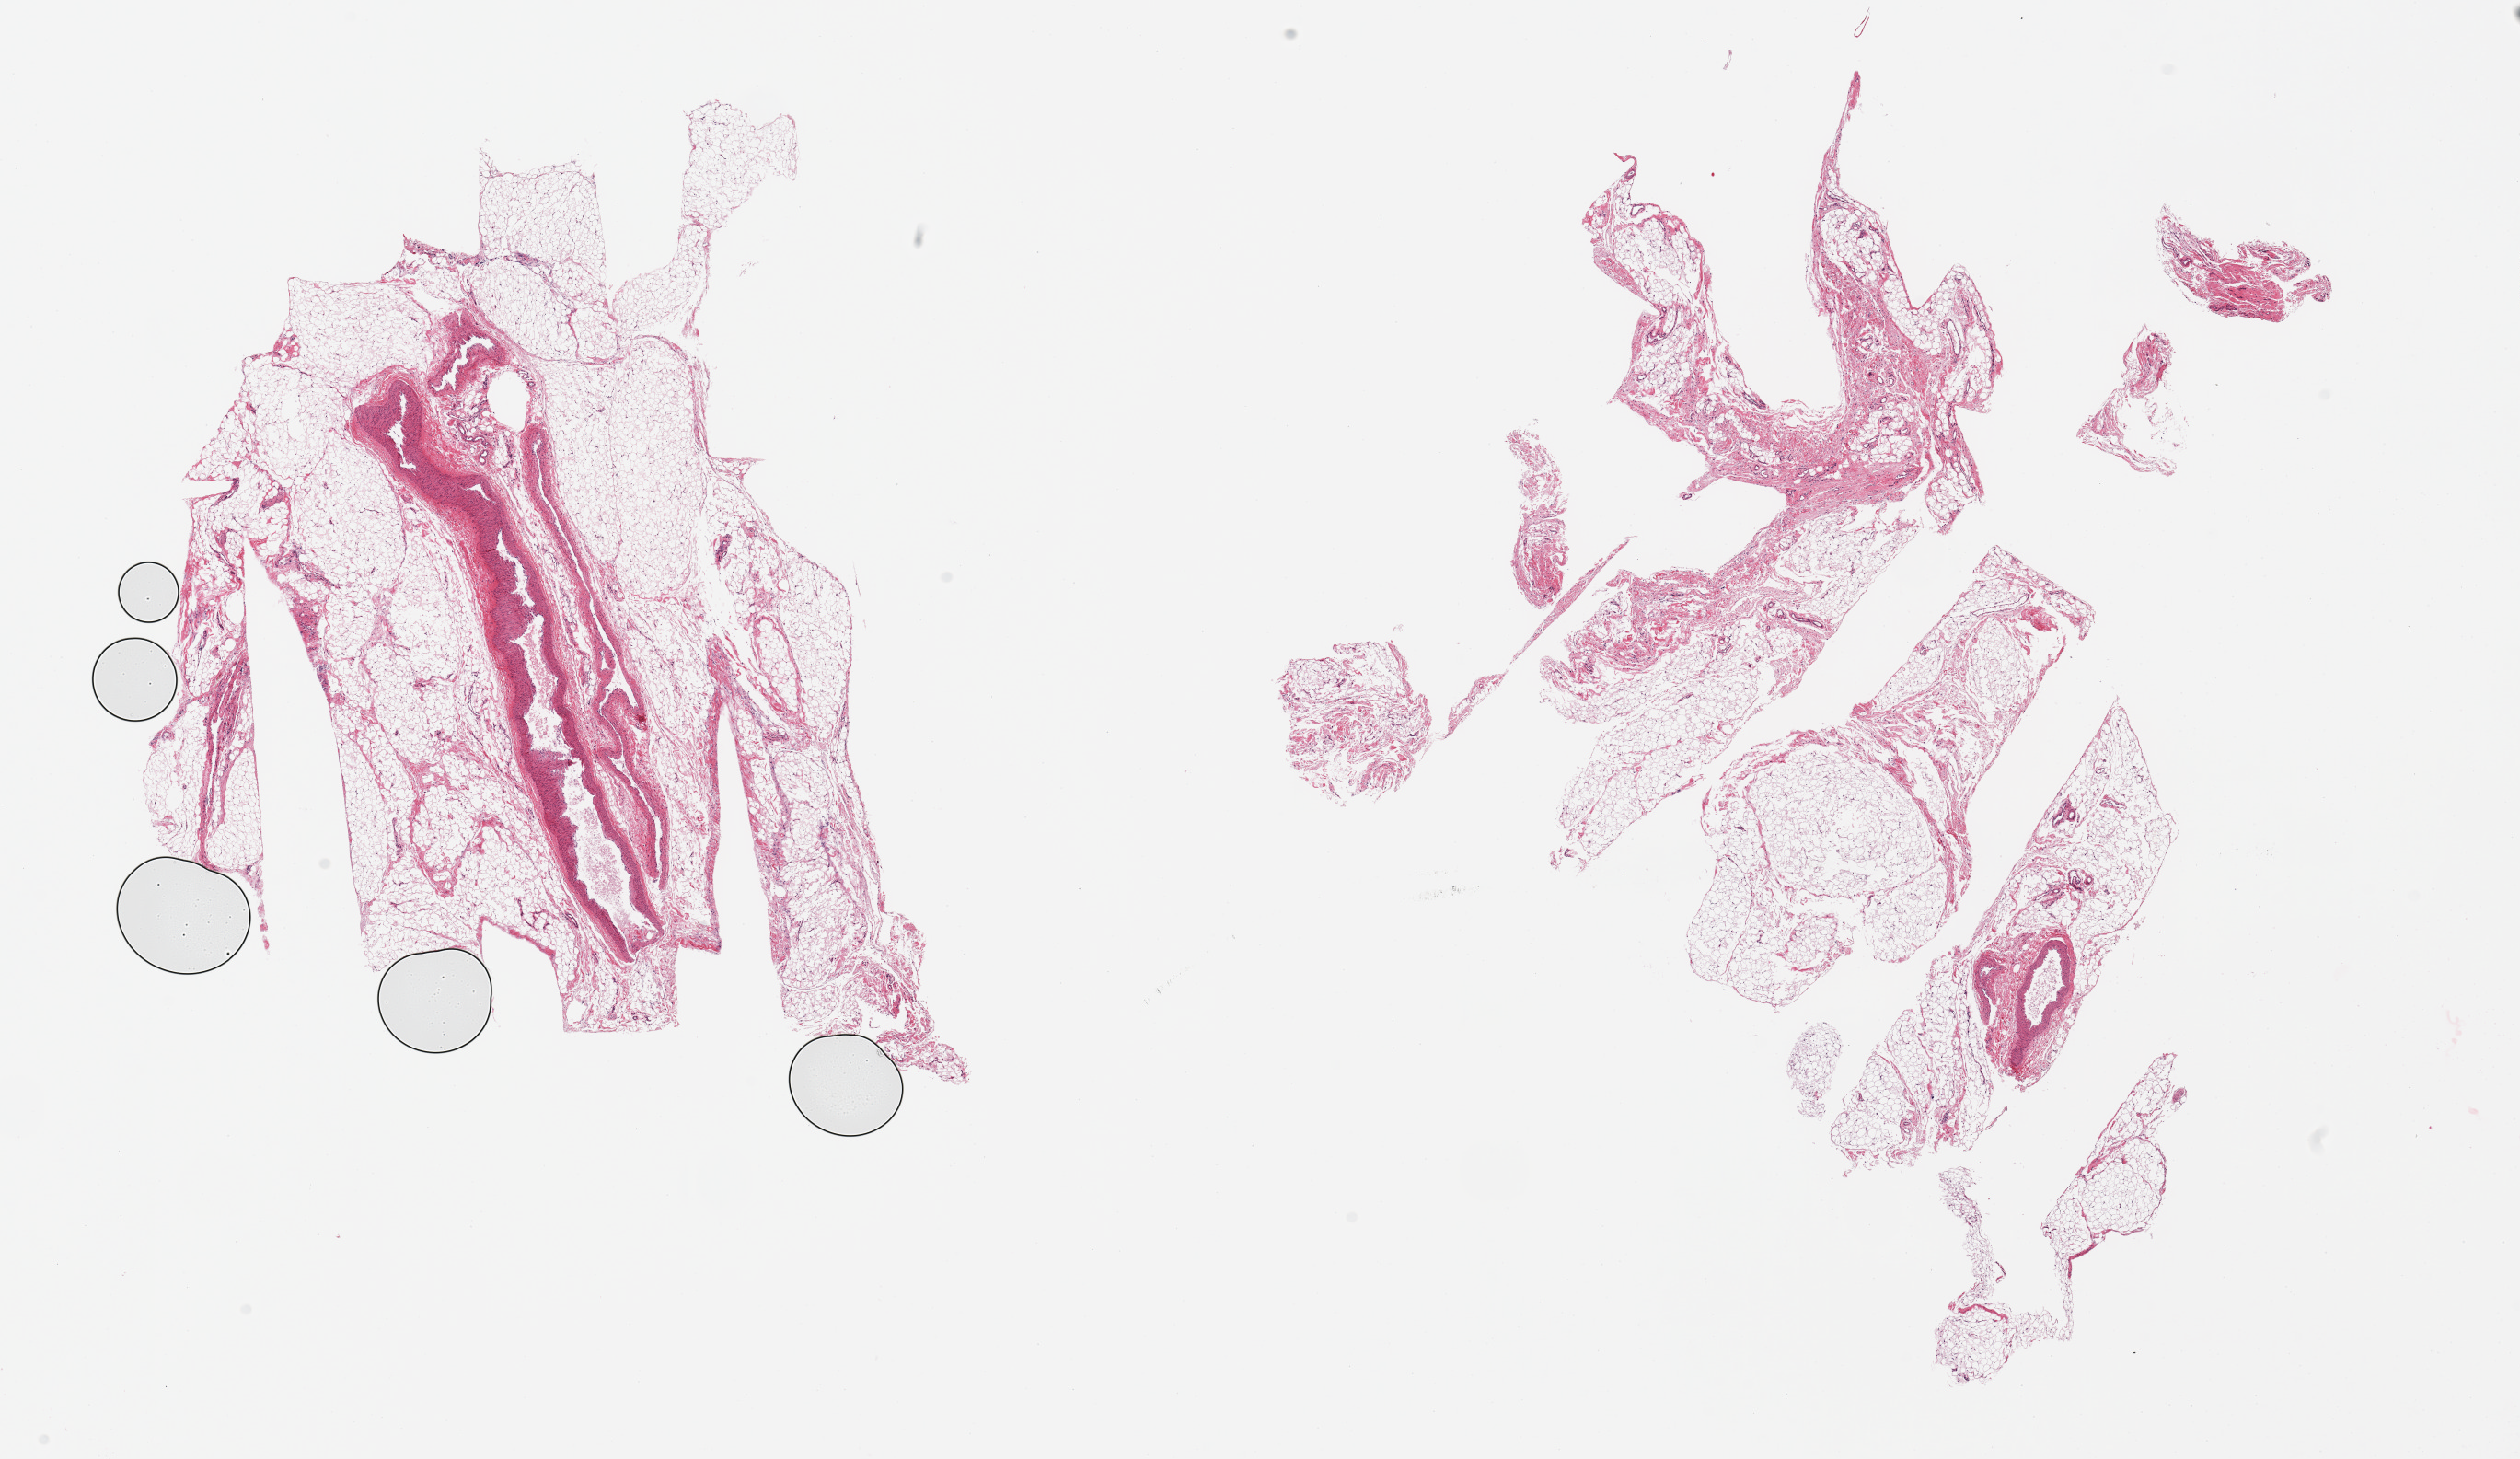
Whole-slide image, haematoxylin and eosin stain, a low-resolution overview of the entire scanned area, about 21.7 x 12.5 mm; PAXgene-fixed, paraffin-embedded tissue; section of omentum (target tissue); tissue donor sample.
Review note (as recorded): 2 pieces; includes several prominent vessels.